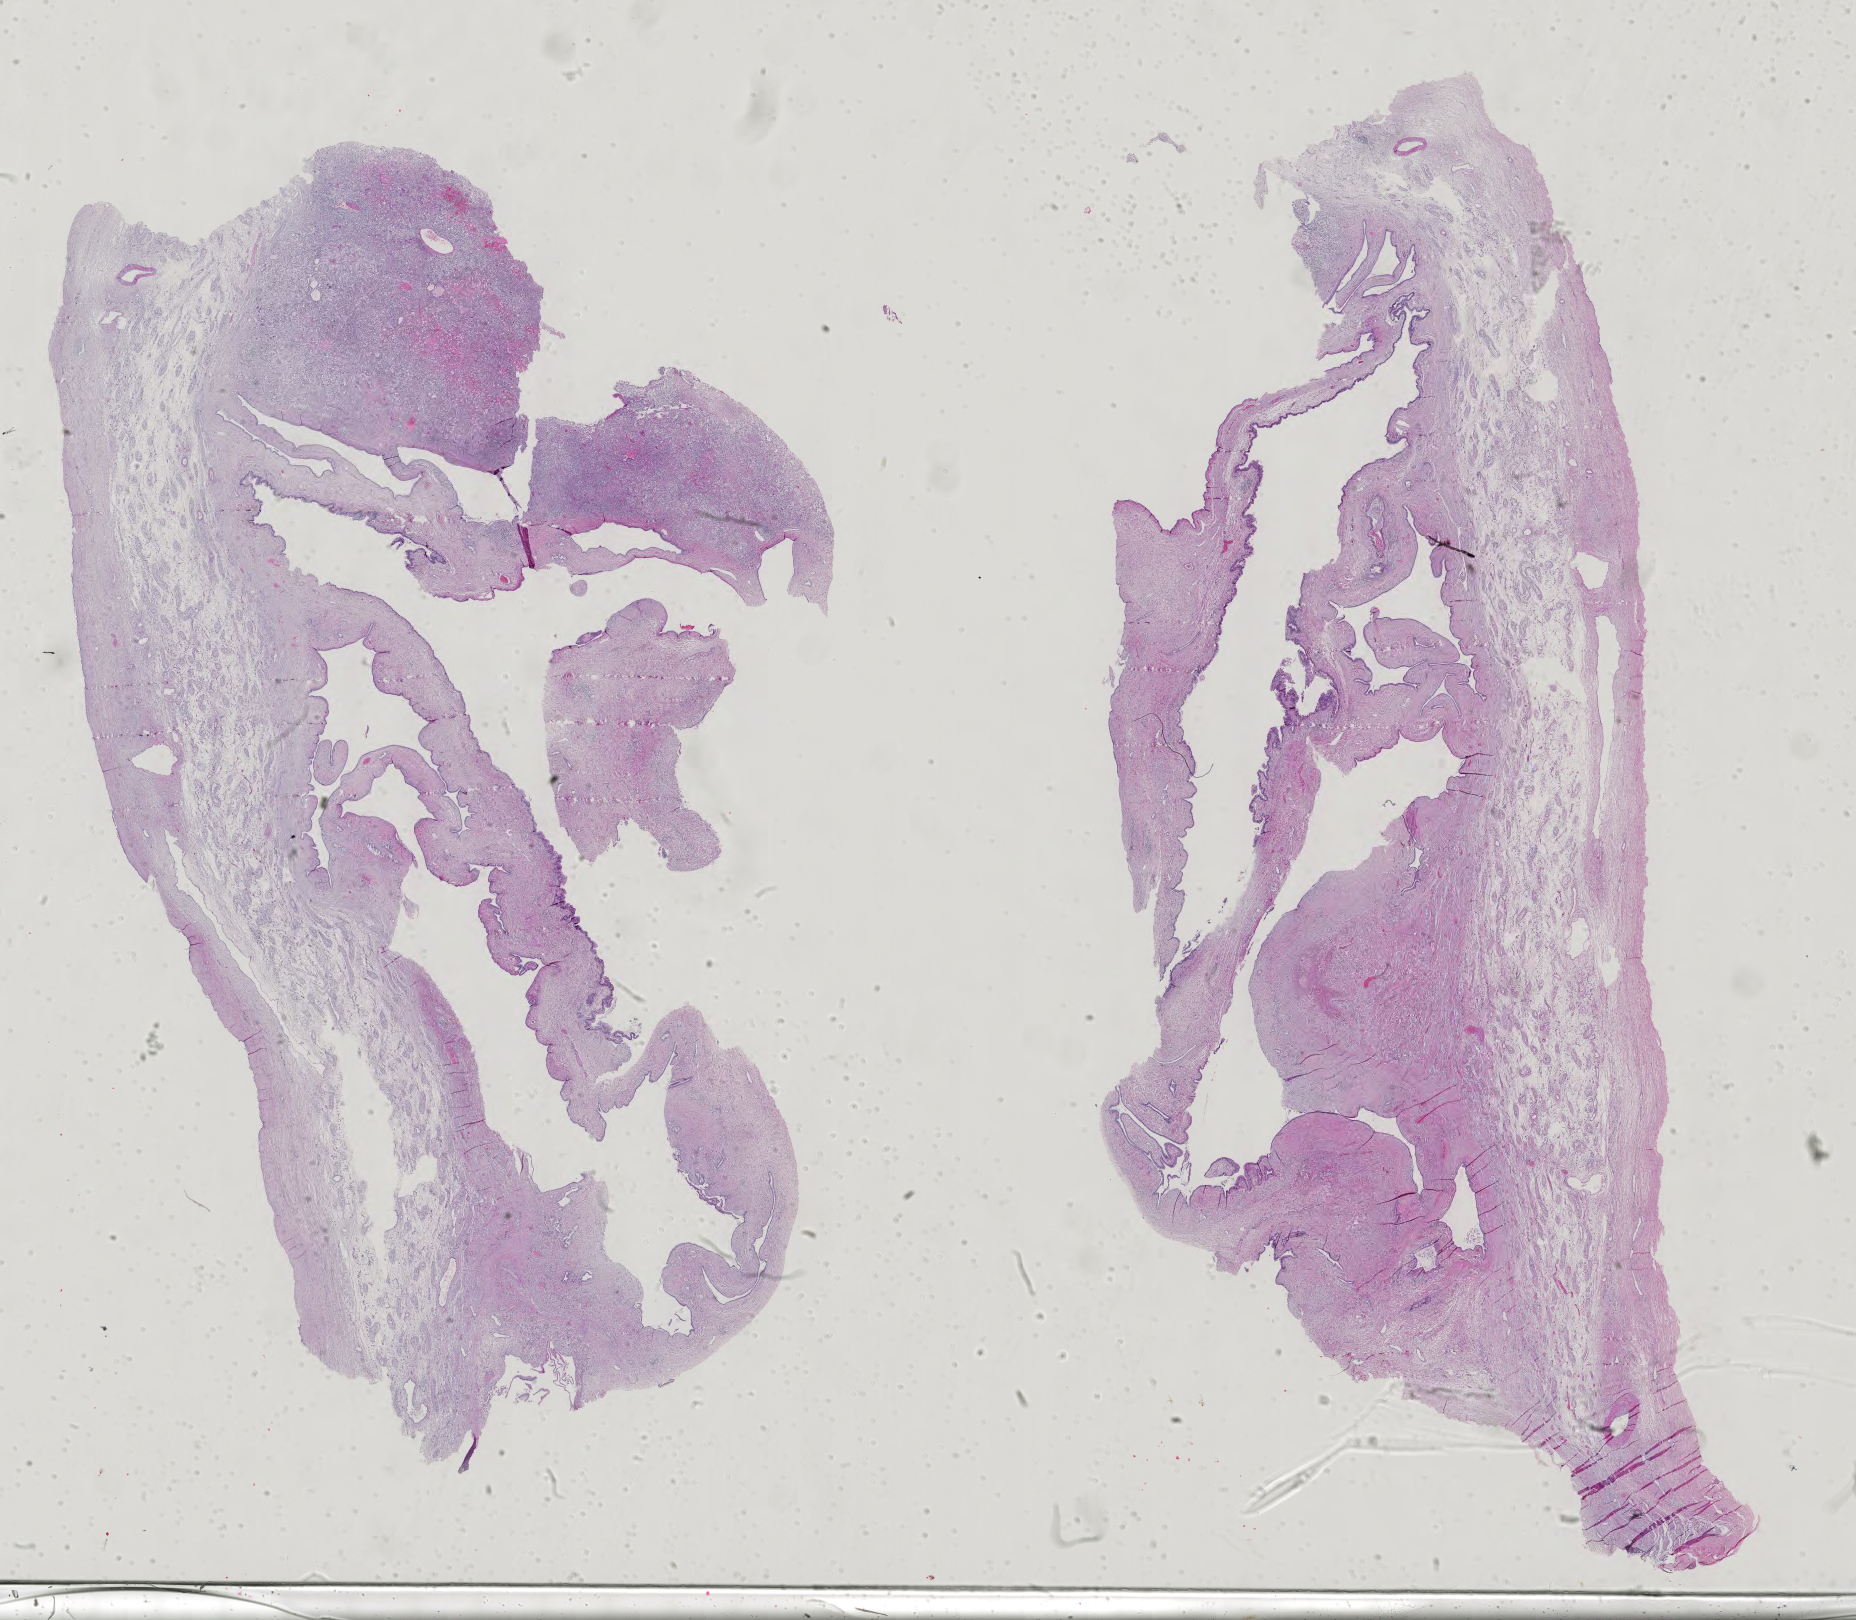
Digitized H&E tissue section (whole slide) — a low-resolution overview of the entire scanned area, about 27.0 x 23.6 mm (acquisition: 40x scan), formalin-fixed paraffin-embedded (FFPE) diagnostic section, sample: primary tumour, testis. Patient: male, age at initial diagnosis 30 years.
Histologic diagnosis: Mixed germ cell tumor. AJCC pathologic stage: IS (5th edition). Laterality: left.